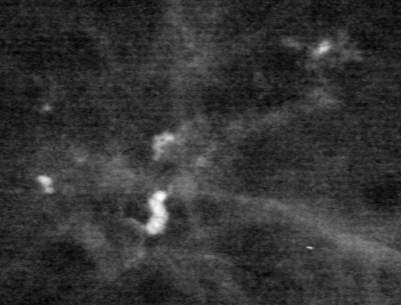
Cropped region of a digitized screen-film mammogram centred on a radiologist-marked abnormality, left breast, CC view.
Finding: calcifications, morphology pleomorphic, distribution clustered; BI-RADS assessment category 4; pathology result (as recorded, not read from the image): benign.